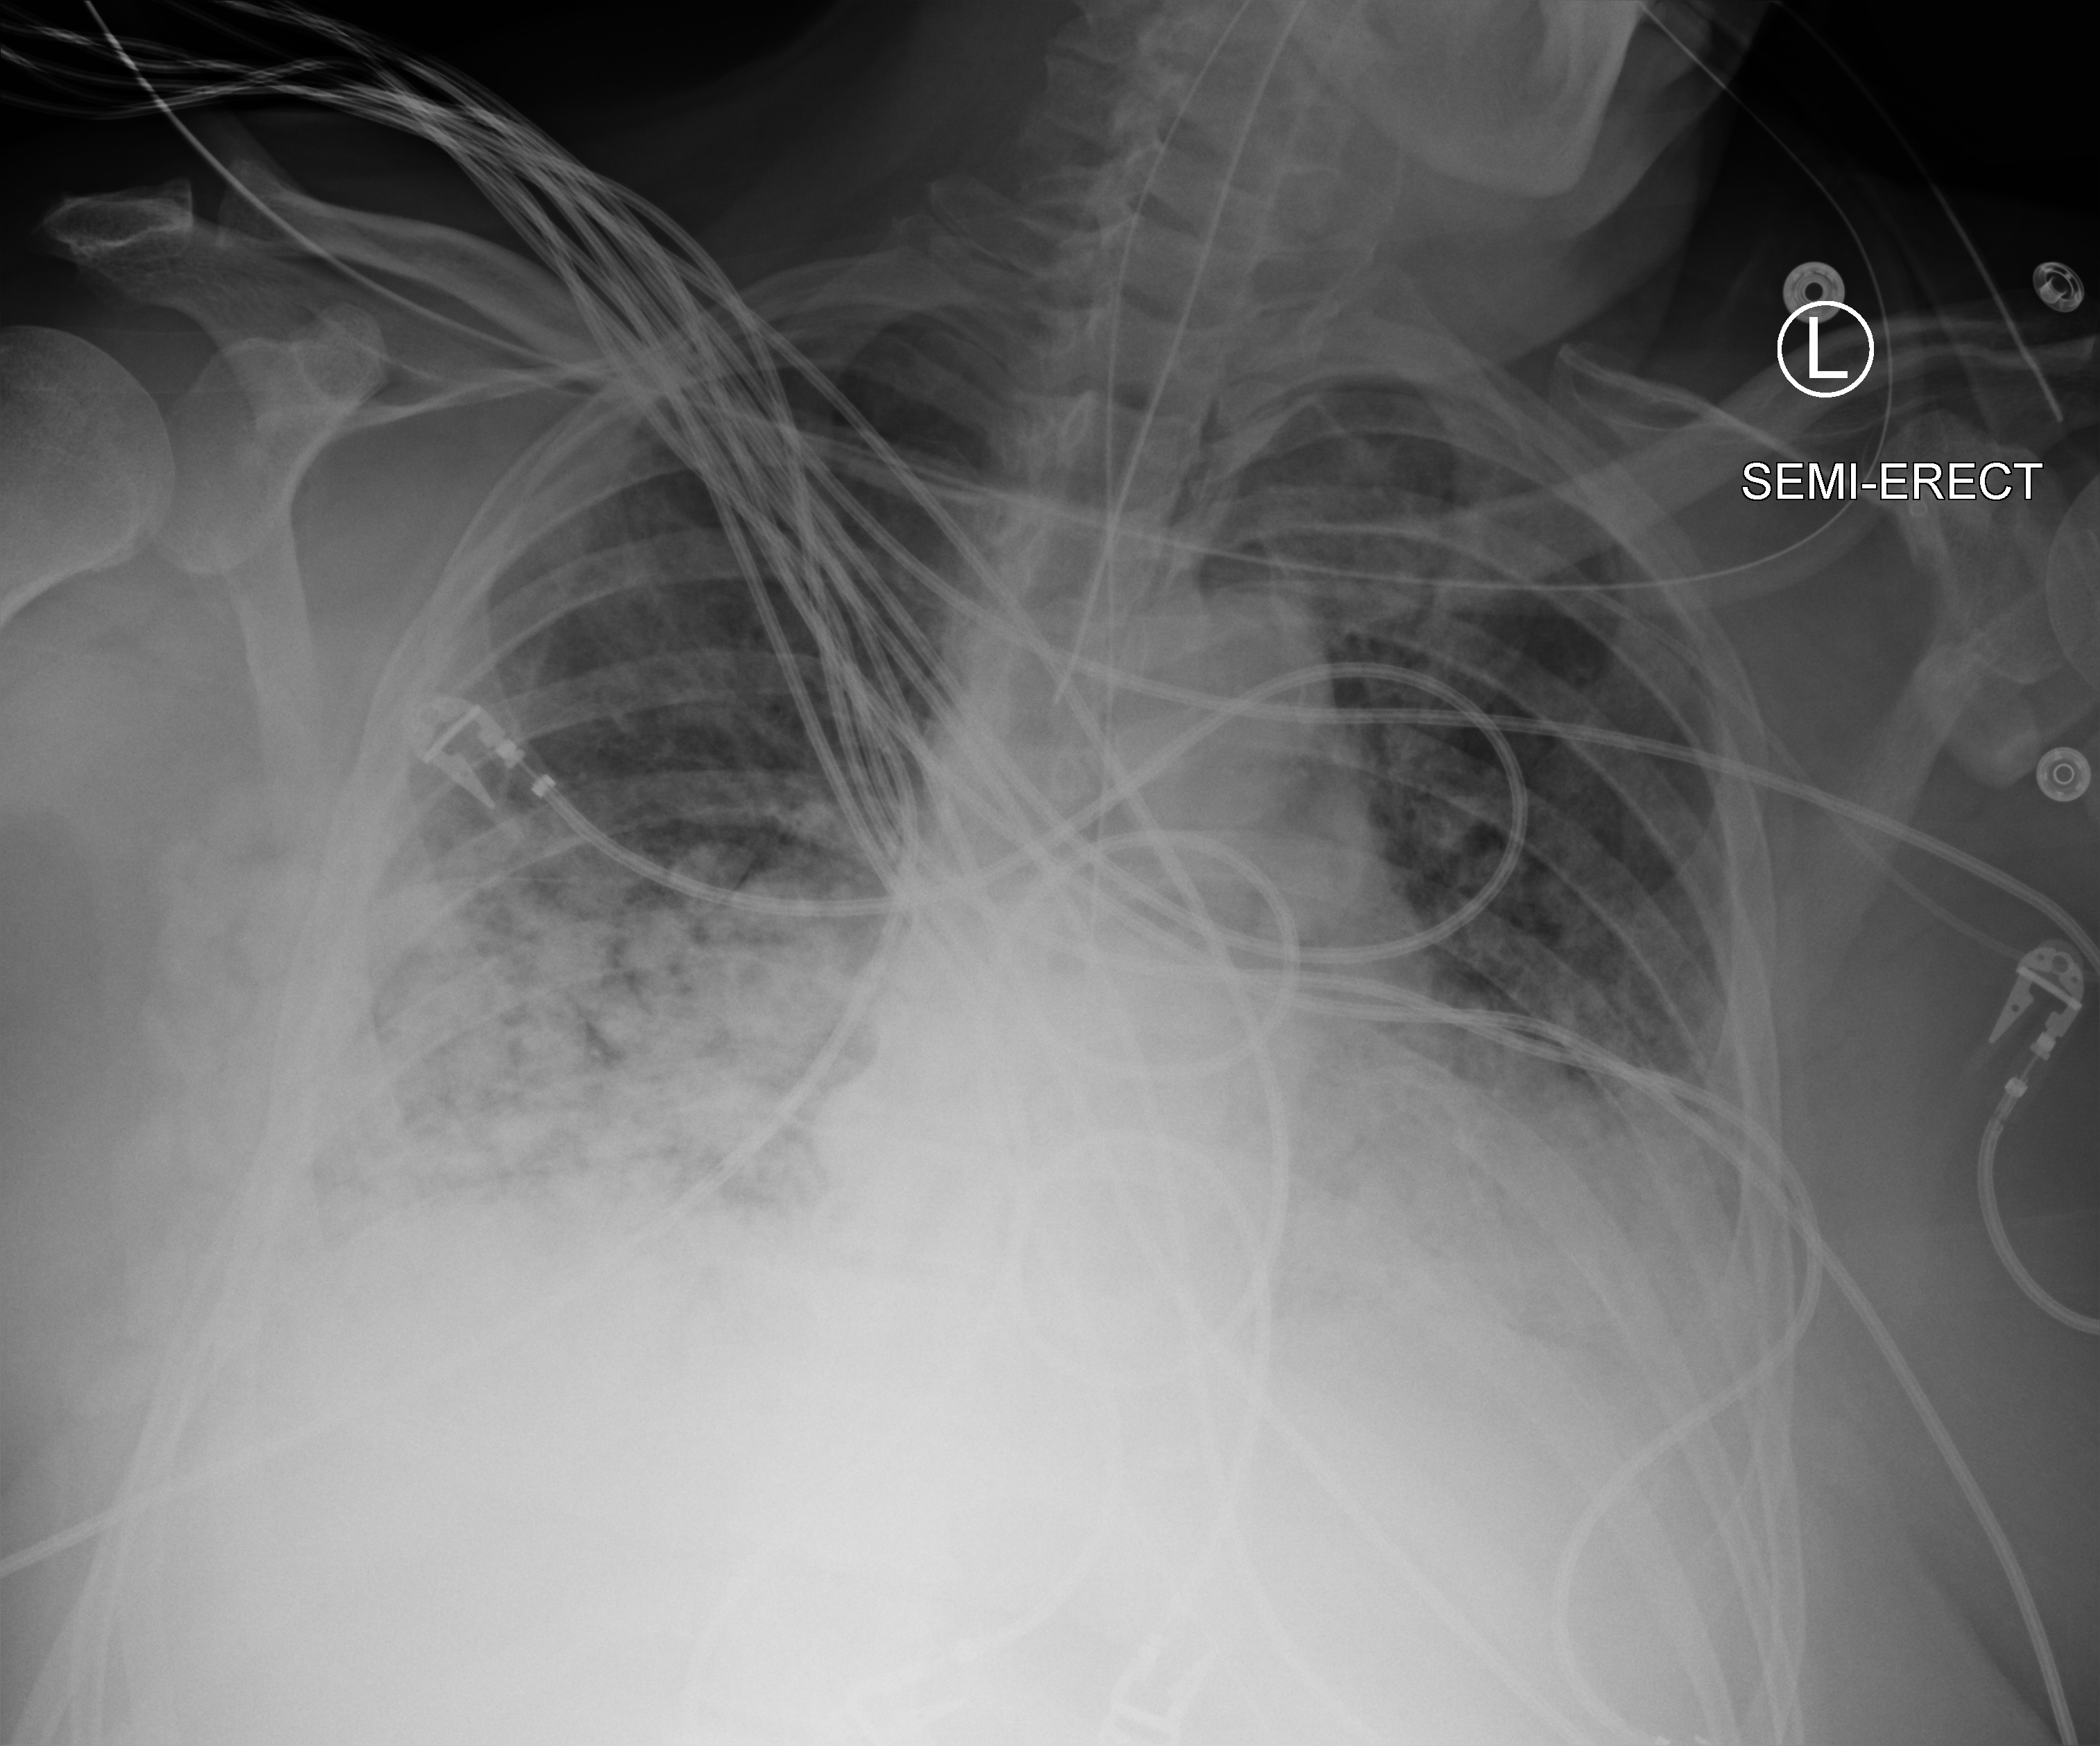
Bedside chest radiograph (computed radiography); anteroposterior (AP) projection. Patient hospitalised with COVID-19; male, aged 60–74 years.
Admission-level facts for this patient (not findings on this image; timing relative to this image not recorded):
- admitted to intensive care during this hospital stay: yes
- mechanically ventilated during this hospital stay: yes